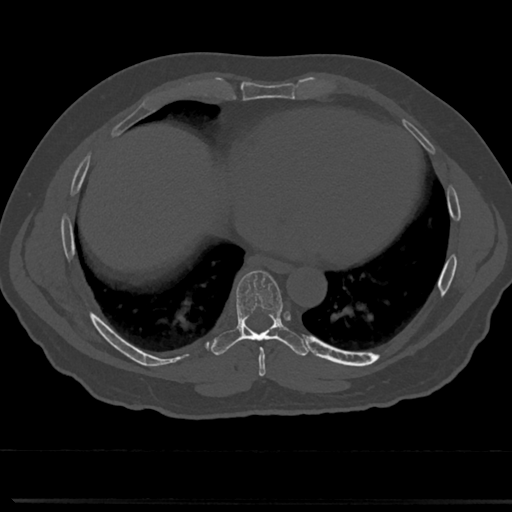
CT including the spine, one axial slice; bone window (W 1800 / L 400 HU); 512 × 512 image matrix, field of view 355 × 355 mm. Male patient, age 61 years. Case-level facts recorded for this patient, not image findings: primary cancer: prostate.
Annotated regions visible in this slice (semi-automatically segmented with operator editing):
- T7 vertebra: bounding box [x1, y1, x2, y2] px = [237, 272, 286, 360]
- T8 vertebra: [237, 272, 283, 336]